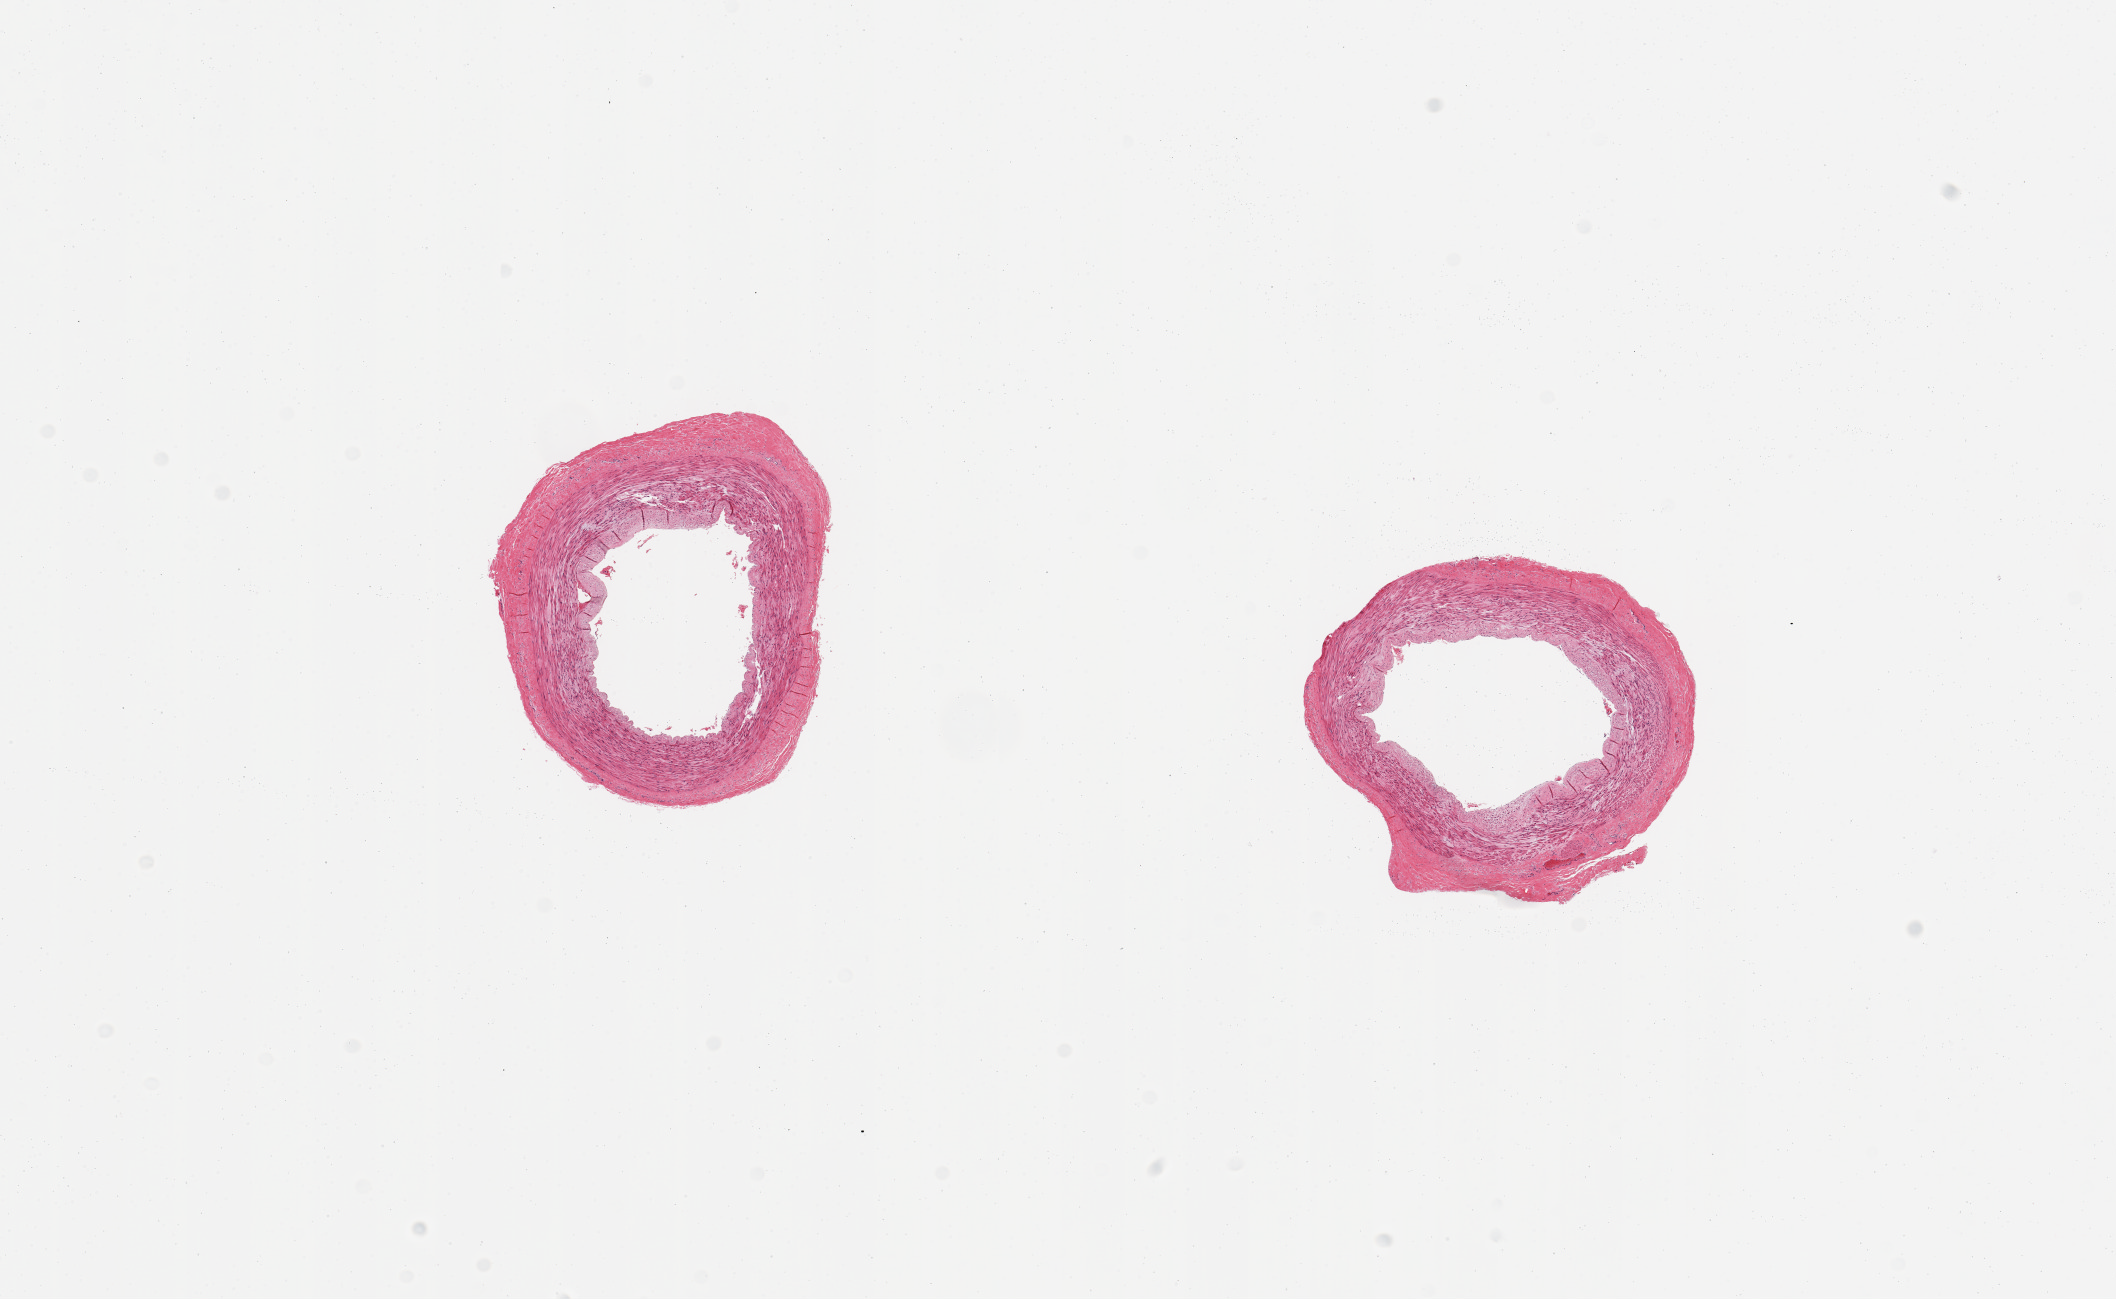
Haematoxylin and eosin whole-slide image, shown as a low-resolution overview of the whole scanned area (about 16.7 x 10.3 mm, from a 20x scan). PAXgene-fixed paraffin-embedded (PFPE) section. Target tissue: tibial artery. Donor tissue sample.
Reviewer comment on this tissue sample: 2 pieces, no fat, excellent clean specimens.